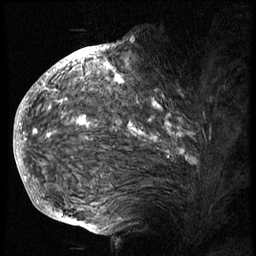
Breast MRI (dynamic contrast-enhanced), one sagittal slice; position 46 of 74 along the scan axis; 3 images stored at this slice position (order not interpretable as contrast timing); 1.5 T; TE 4.2 ms, TR 8.9 ms; 2.5 mm slice thickness; 256 × 256 image matrix, field of view 200 × 200 mm. Female patient, age 57 years. Case-level facts recorded for this patient, not image findings: setting: breast cancer imaged before/during neoadjuvant chemotherapy; receptor status: HER2-positive.
Structures marked on this image (semi-automatic segmentation, software-assisted and operator-edited):
- analysis volume of interest (the breast-tissue region the enhancement analysis was run in; not a lesion): bounding box <40,62,242,175> (left, top, right, bottom; pixels)
- tumour enhancement mask (voxels above the 140 % enhancement threshold inside the analysis volume of interest): <41,63,186,158>